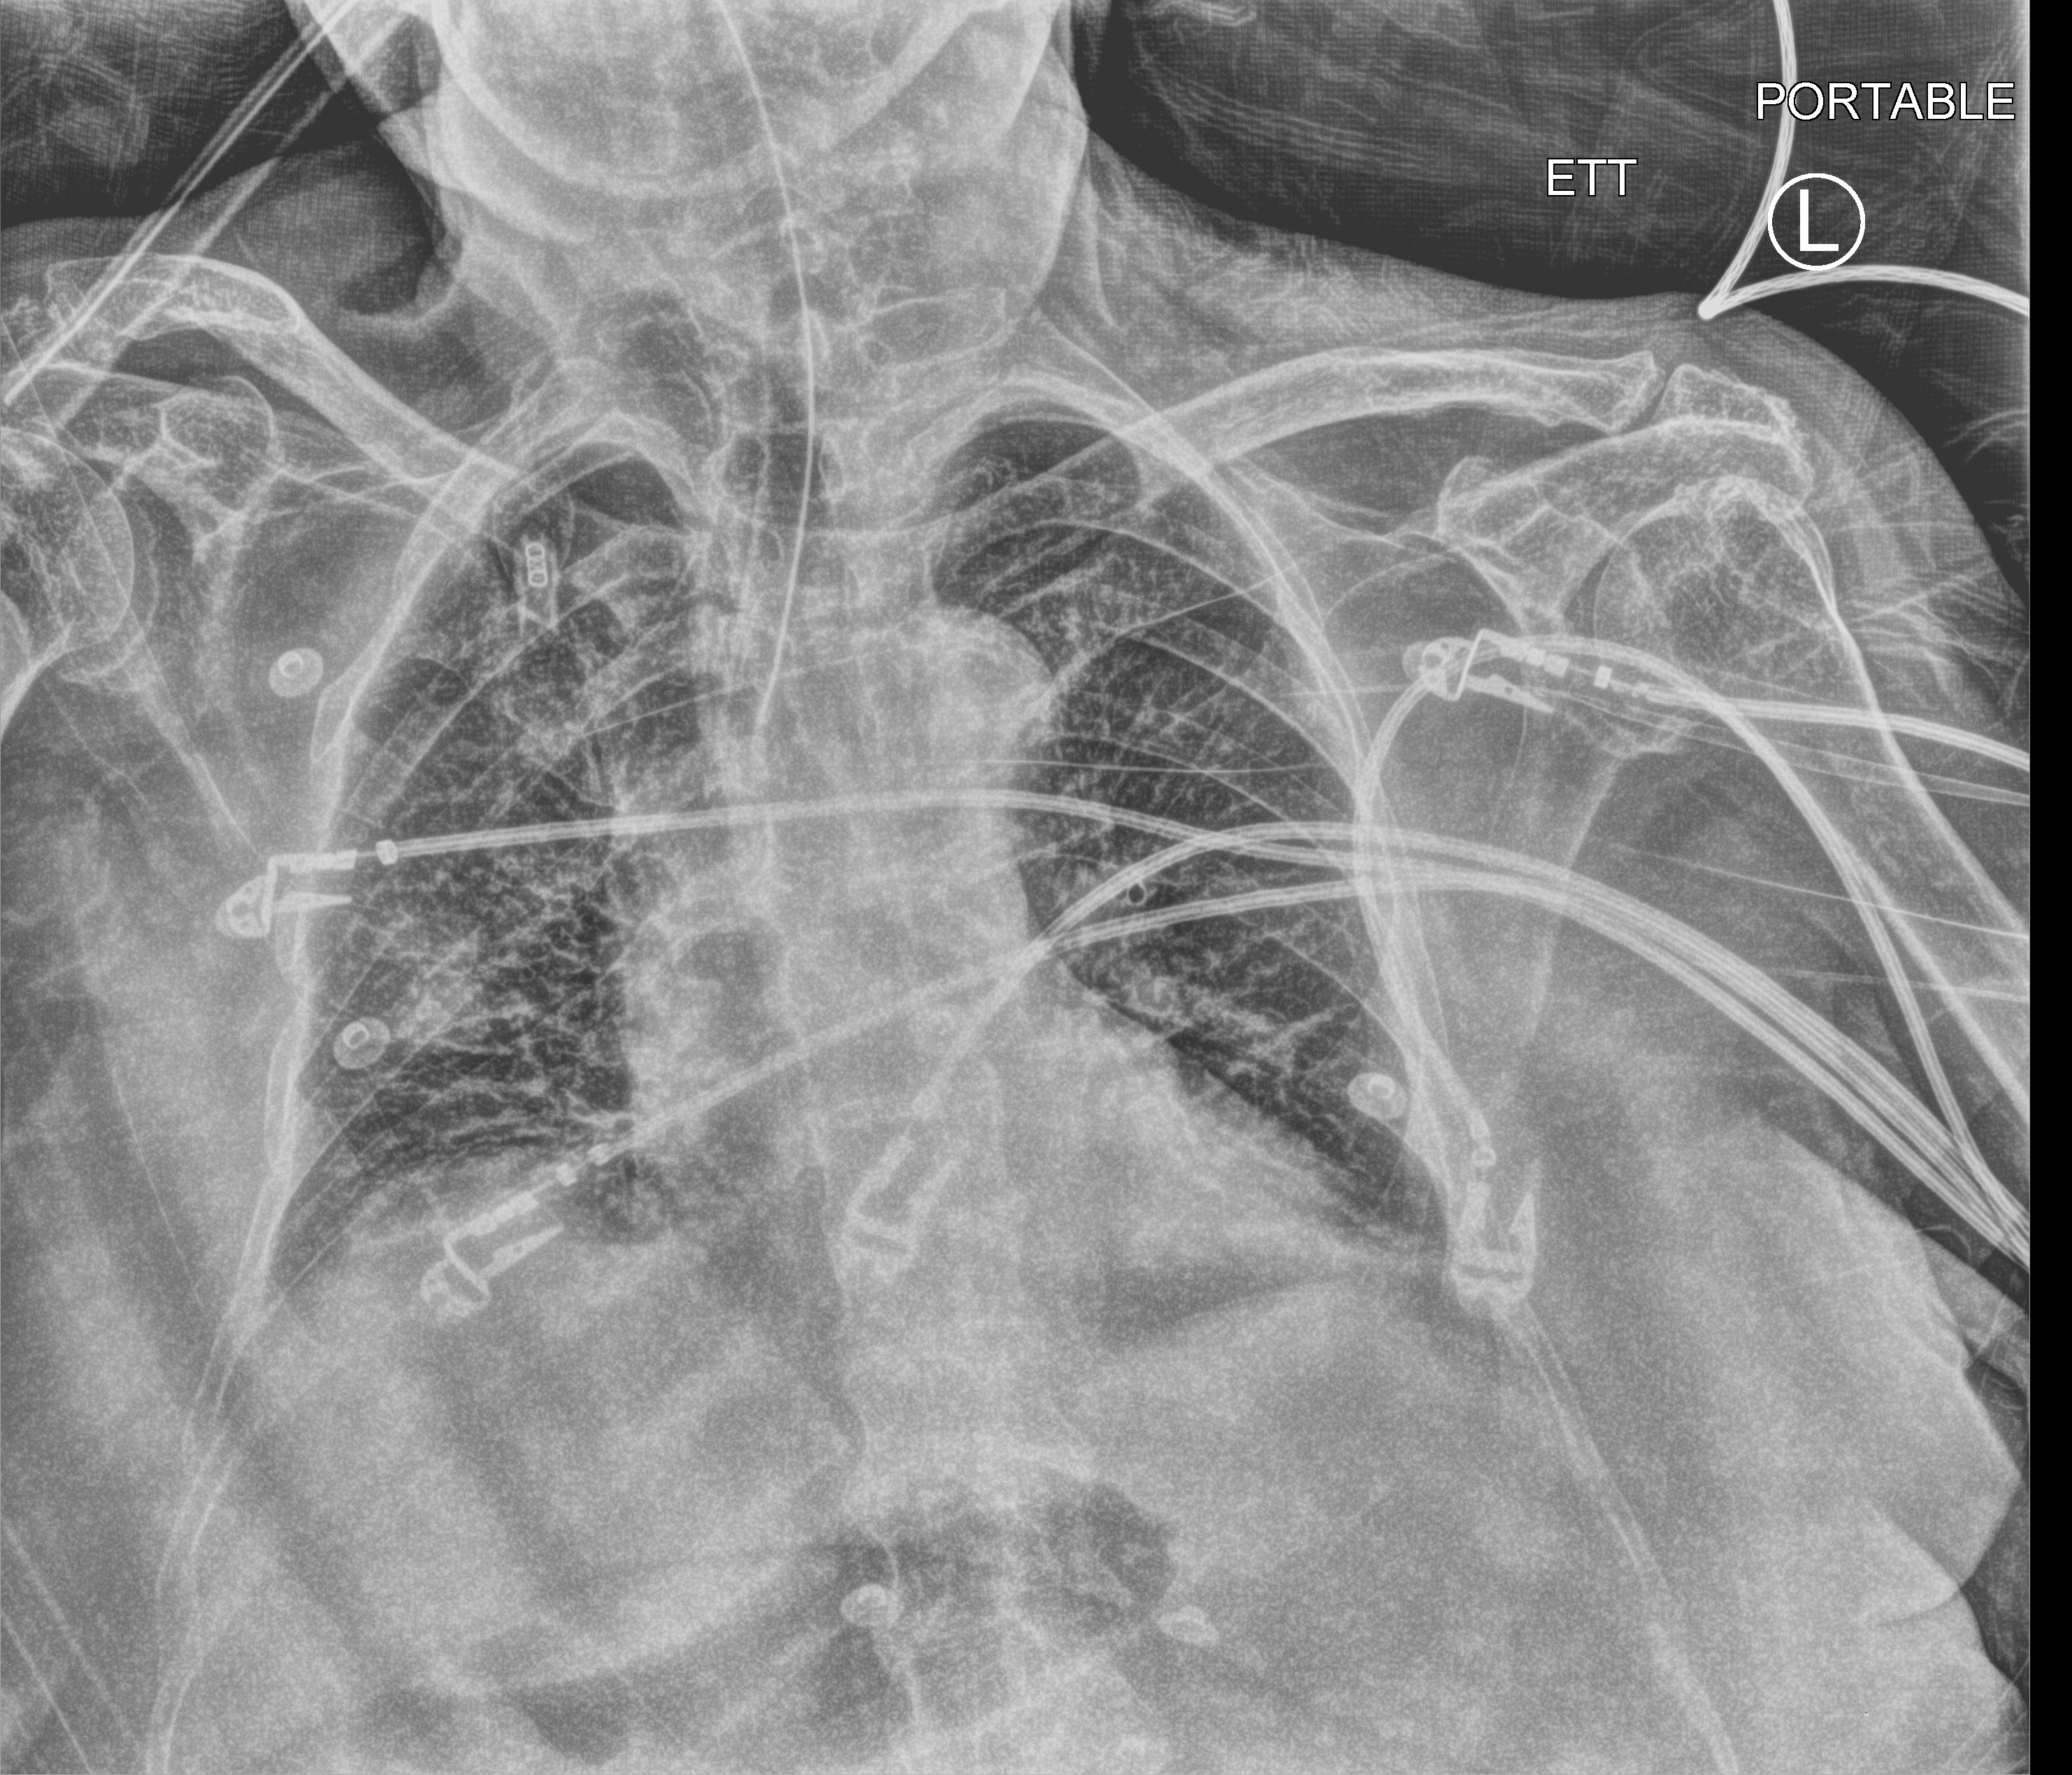
Chest X-ray (portable); anteroposterior (AP) projection. Patient hospitalised with COVID-19; female, aged 75–90 years.
From the hospital-stay record, not from the radiograph (when in the stay this image was taken is not recorded):
- mechanically ventilated during this hospital stay: yes
- diabetes (admission record): no
- admitted to intensive care during this hospital stay: yes